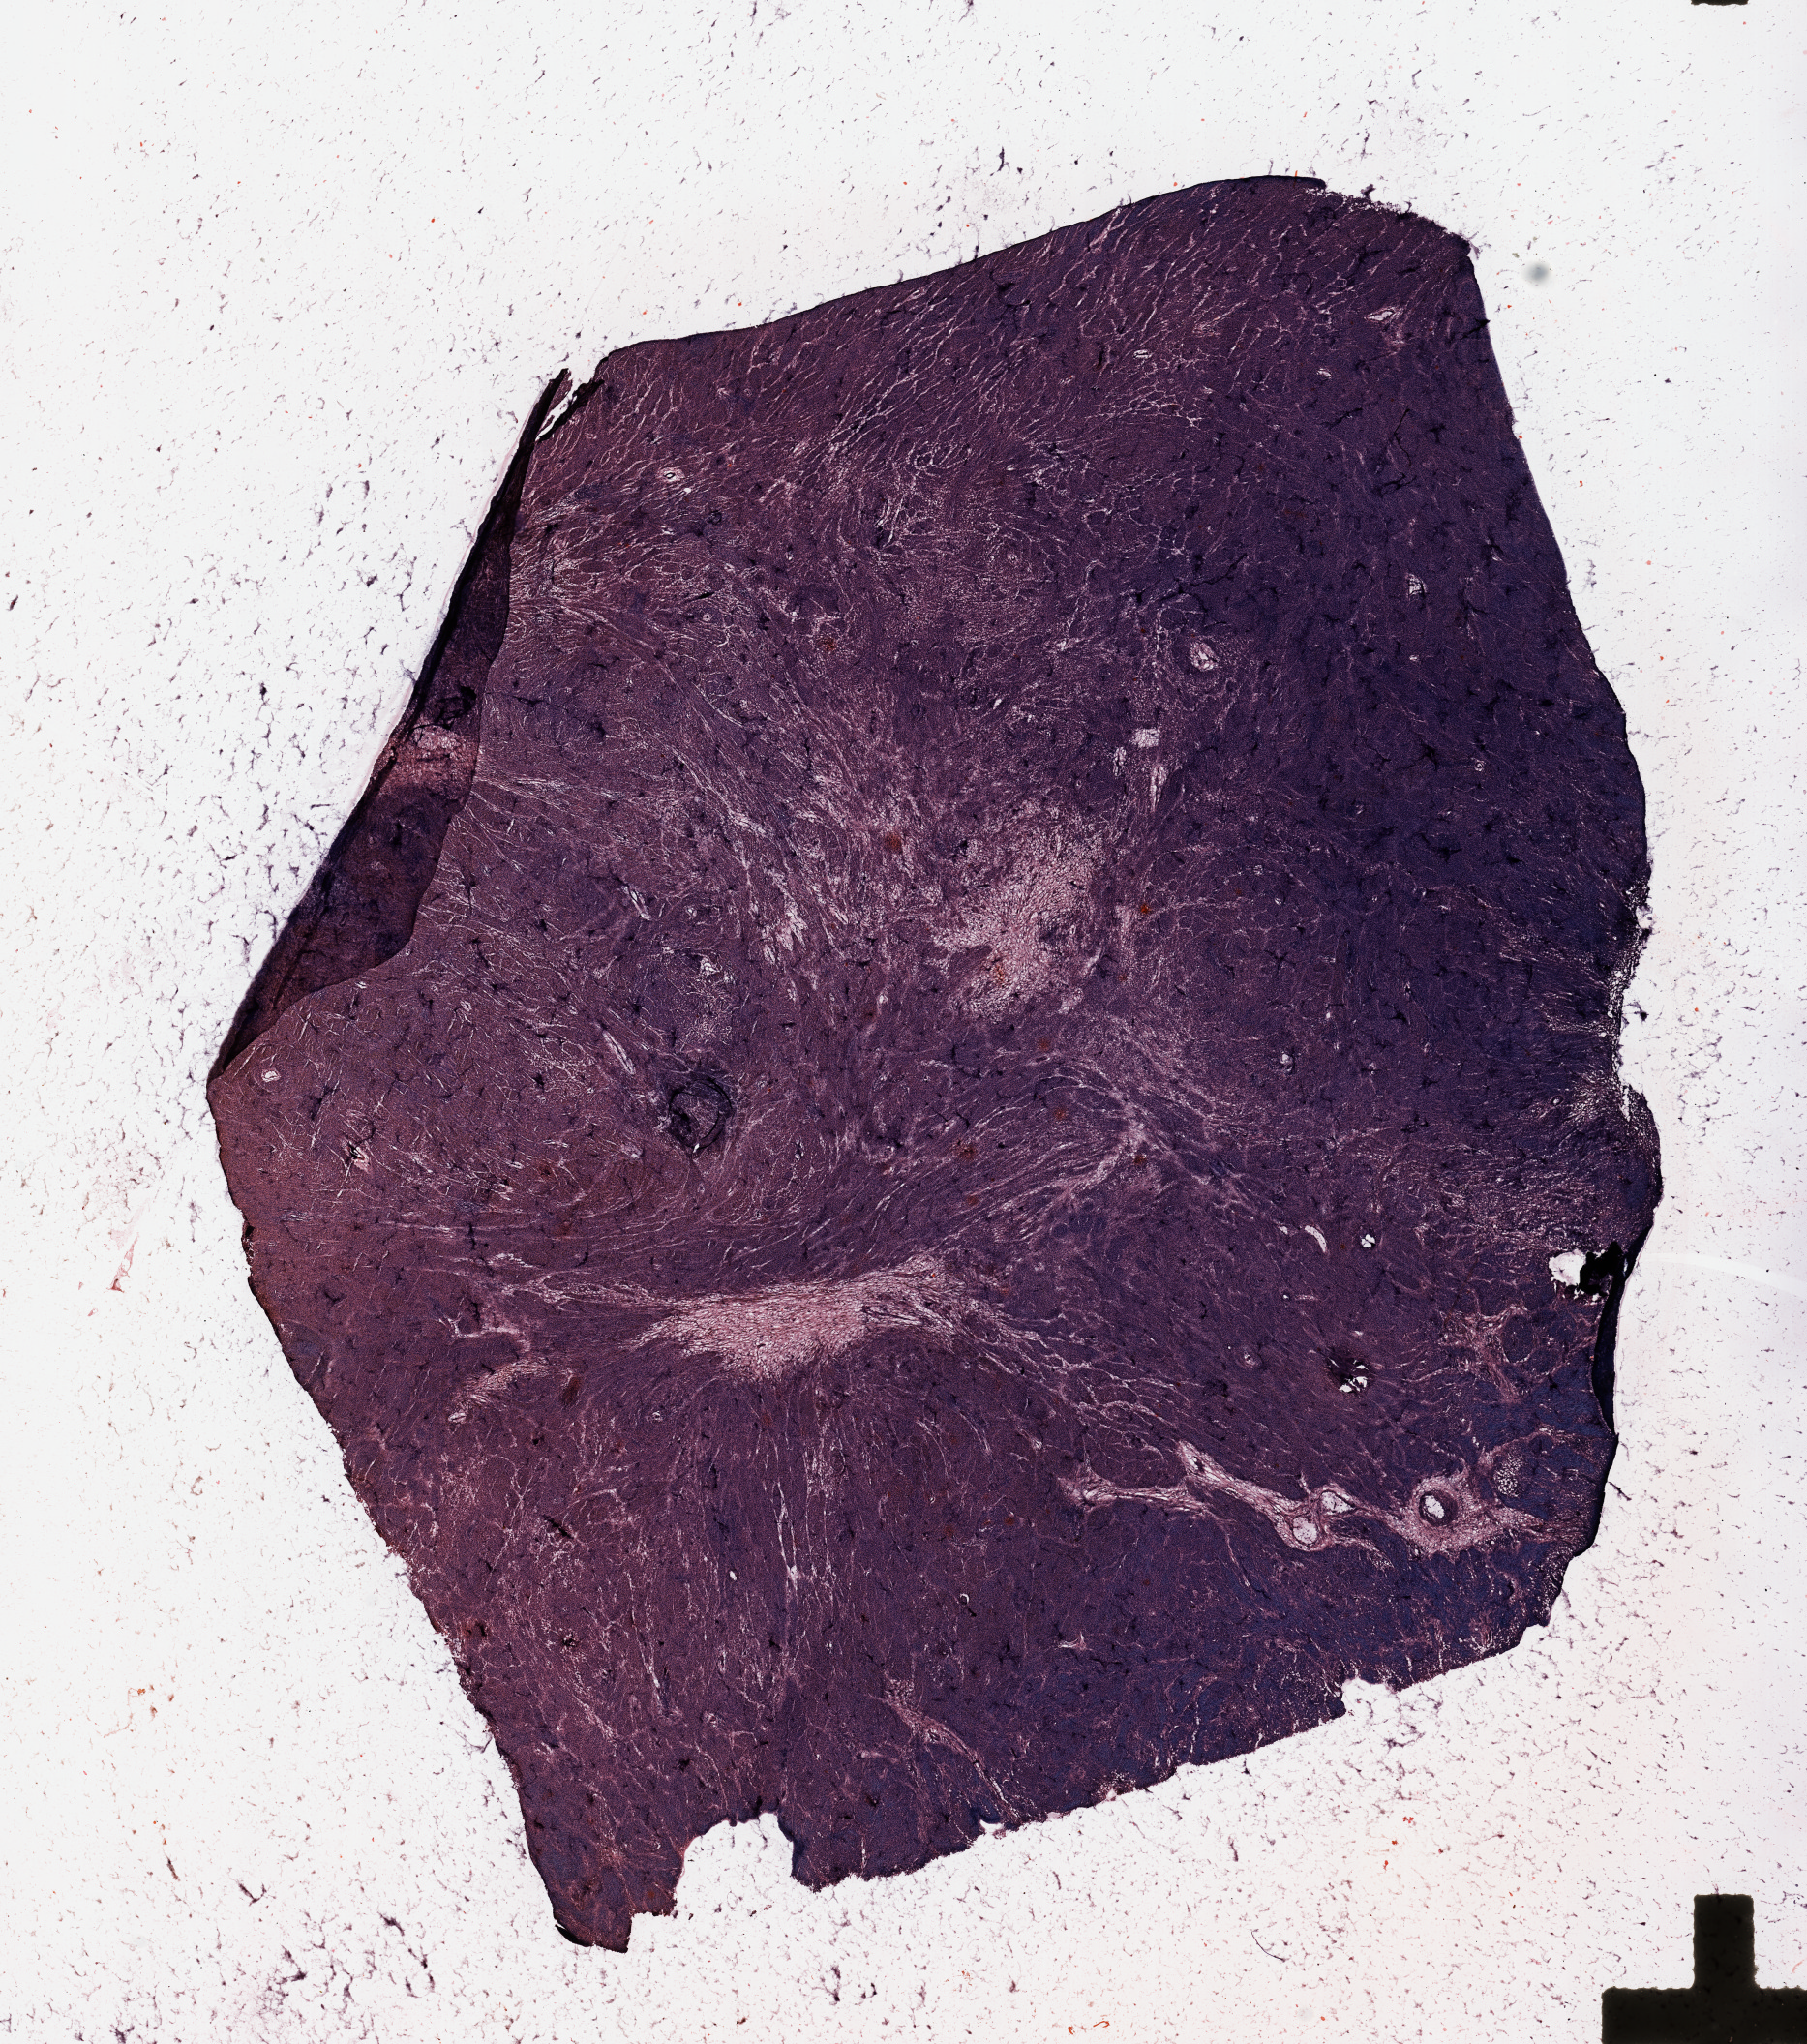
Digitized Hematoxylin and eosin (H&E) stained tissue section (whole slide) — low-resolution overview of the scanned area, about 14.8 x 16.7 mm (from a 20x scan), melanoma tumour tissue; sampled site not recorded. Female, 67 y/o.
Patient diagnosis (cohort enrolment): cutaneous melanoma (skin). Primary tumour site (as recorded): extremities.